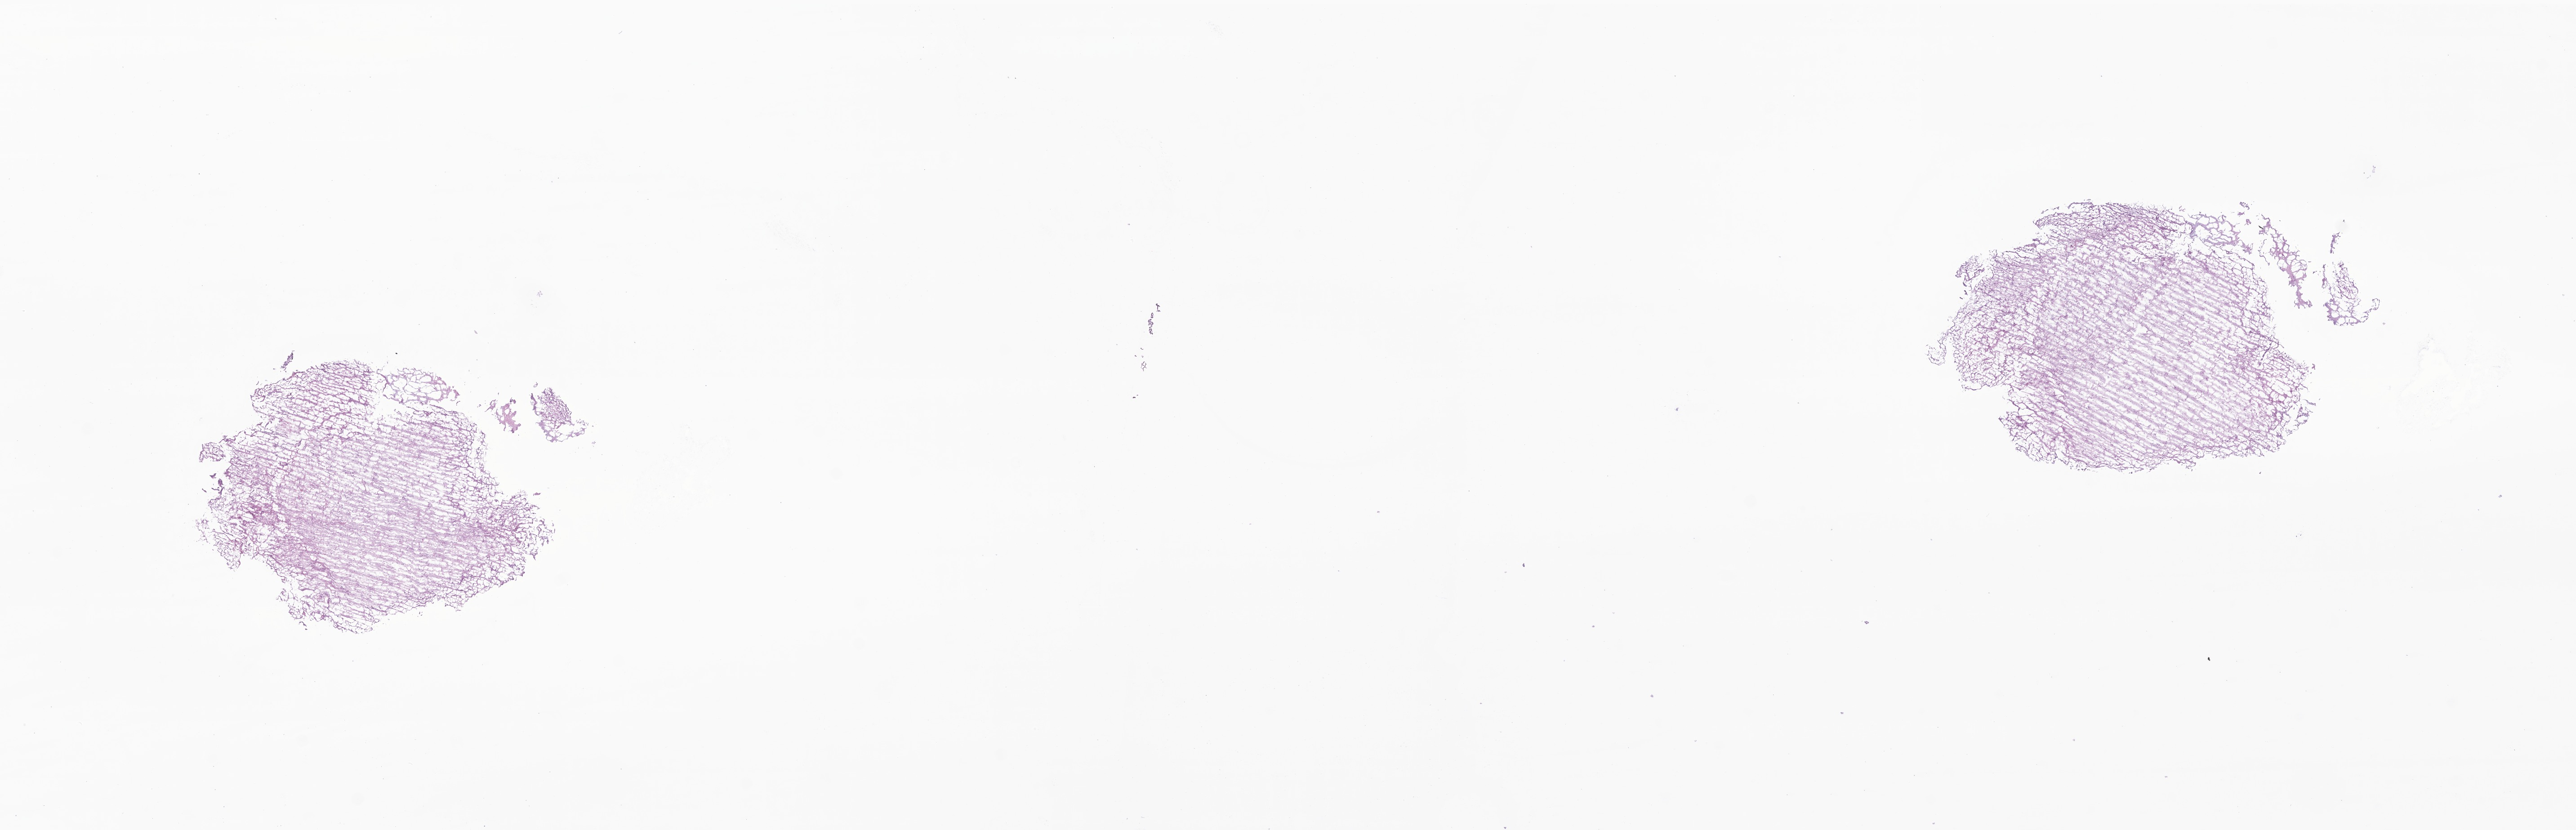
Haematoxylin and eosin whole-slide image of tumor tissue from the brain, whole scanned area (about 24.2 x 7.8 mm) shown as a low-resolution overview. Frozen section. Patient: male, age 113 months (9 years 5 months).
Recorded diagnosis: Pilocytic astrocytoma.